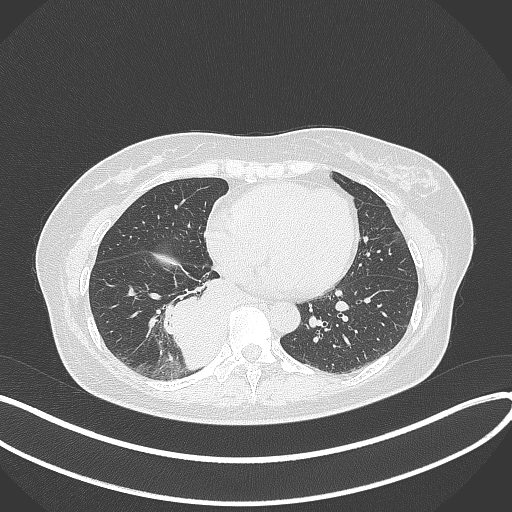
Chest CT, one axial slice. Position 130 of 331 along the scan axis. Reconstruction kernel B70f. Lung window (W 1500 / L -600 HU). 1 mm slice thickness. 512 × 512 image matrix, field of view 400 × 400 mm. Female patient, age 54 years. Case-level facts recorded for this patient, not image findings: clinical TNM (as recorded): T4 N0 M0.
Annotated regions visible in this slice (rectangle marked by the reading radiologist):
- lung tumour (recorded histology: adenocarcinoma): box from (x=164, y=262) to (x=233, y=372) px